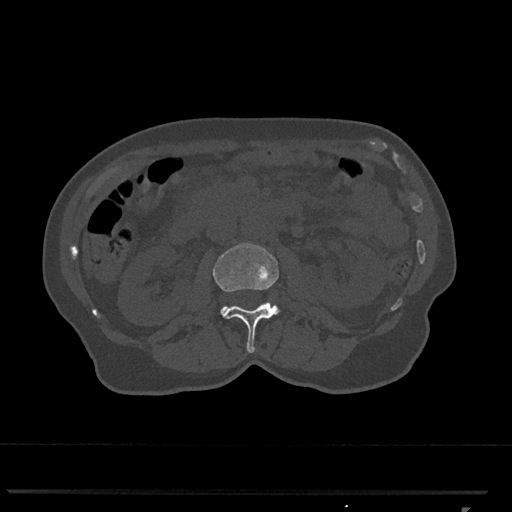
CT including the spine, one axial slice. Position 326 of 793 along the scan axis. 120 kVp. Bone window (W 1800 / L 400 HU). 512 × 512 image matrix, field of view 380 × 380 mm. Patient: female, 62 years. Case-level facts recorded for this patient, not image findings: primary cancer: renal.
Structures marked on this image (semi-automatic segmentation, software-assisted and operator-edited):
- L2 vertebra: bounding box (x1, y1, x2, y2) in pixels: (213, 243, 280, 353)